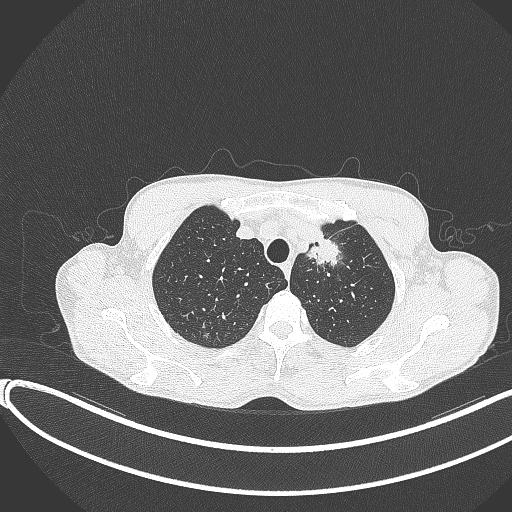
Chest CT, one axial slice. Slice 324 of 374 in the series (ordered by position). Reconstruction kernel B70f. 120 kVp. Lung window (W 1500 / L -600 HU). 1 mm slice thickness. 512 × 512 image matrix, field of view 400 × 400 mm. Patient: male, 58 years. Case-level facts recorded for this patient, not image findings: clinical TNM (as recorded): T1c N1 M0.
Structures marked on this image (bounding box drawn by a radiologist):
- lung tumour (recorded histology: adenocarcinoma): bounding box [x1, y1, x2, y2] px = [298, 224, 342, 274]